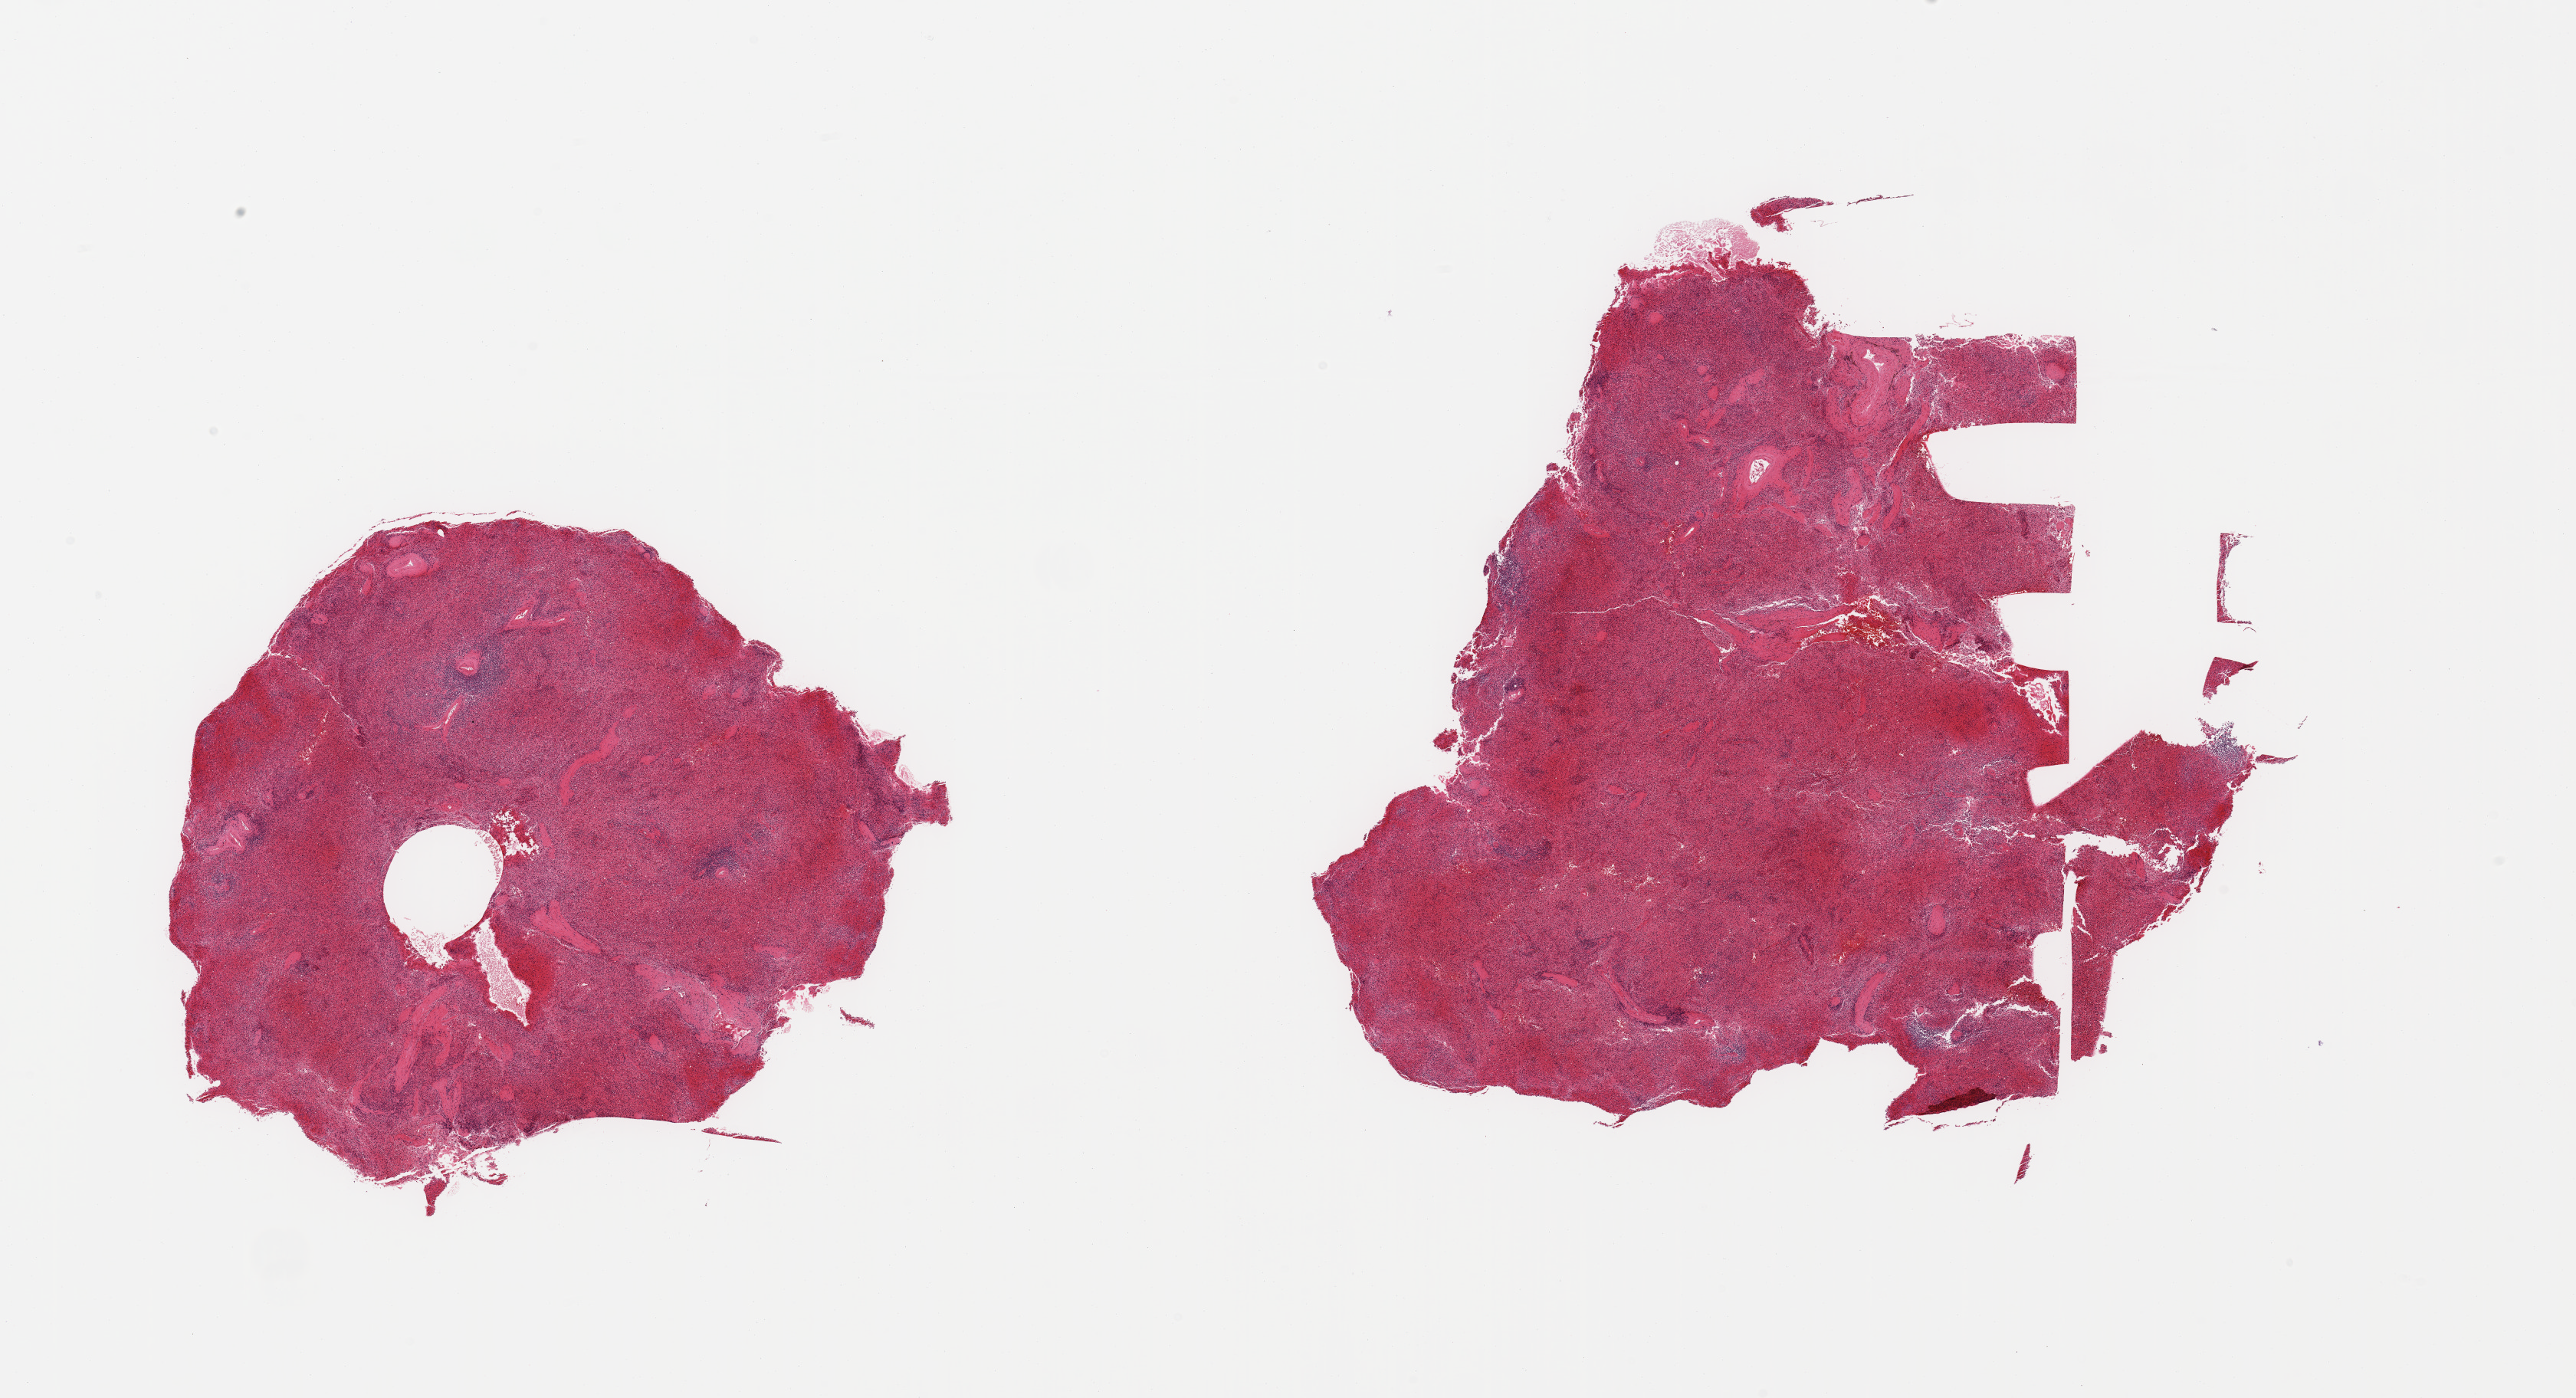
Whole-slide image, haematoxylin and eosin stain, shown as a low-resolution overview of the whole scanned area (about 26.6 x 14.4 mm), PAXgene-fixed, paraffin-embedded tissue, section of spleen (target tissue), donor tissue sample. Female donor.
Pathologist's review note for this sample: 2 pieces, moderate-marked congestion.